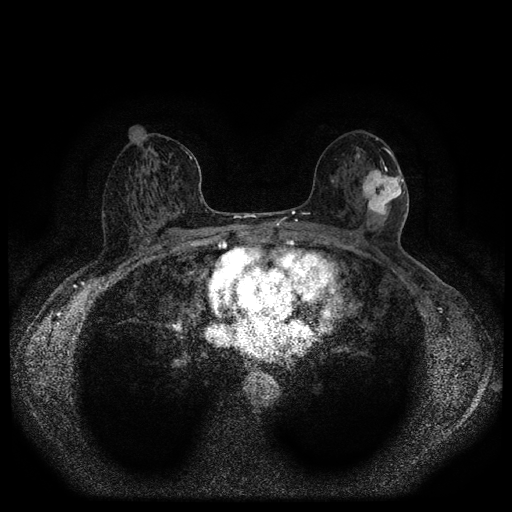
Breast MRI (dynamic contrast-enhanced, multi-phase), one axial slice; position 56 of 116 along the scan axis; dynamic contrast-enhanced series, time point 2 of 5 at this slice position (early post-contrast); 1.5 T; TE 2.7 ms, TR 5.4 ms; 512 × 512 image matrix, field of view 330 × 330 mm. Female patient, age 56 years.
Structures marked on this image (semi-automatically segmented with operator editing):
- breast lesion (labelled 'tumour' in the annotation; benign lesions carry a separate 'benign' label): bounding box [x1, y1, x2, y2] px = [361, 167, 406, 220]